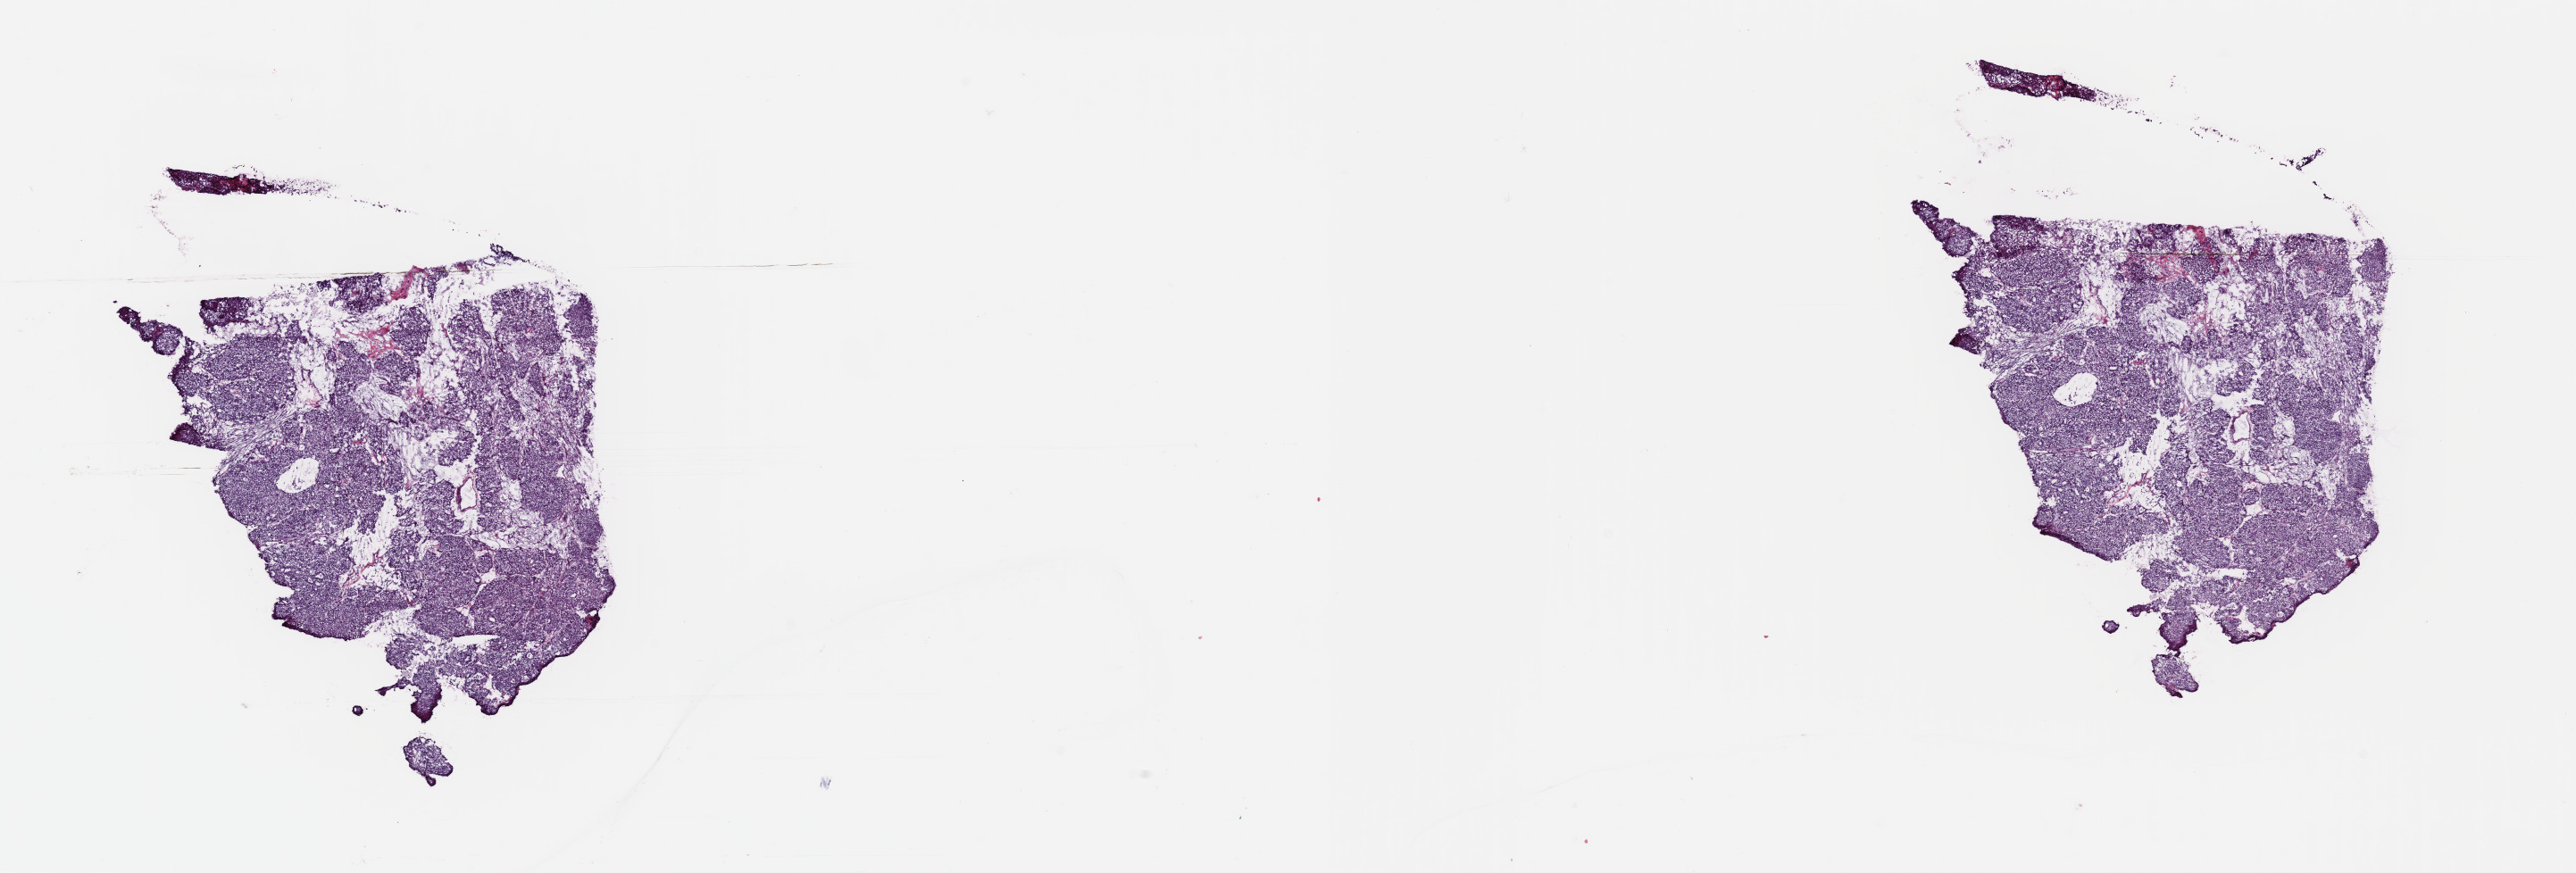
Digitized Hematoxylin and eosin (H&E) stained tissue section (whole slide) — low-resolution overview of the scanned area, about 22.8 x 7.7 mm, frozen section from the top of the tissue portion, uterus, primary tumour sample. Female, age 86 years at initial diagnosis. Histologic grade: G3 (poorly differentiated). Composition of this section per pathologist review: tumour cells 80%, tumour nuclei 80%, normal cells 0%, stromal cells 18%, necrosis 2%. Infiltration values recorded for this section: lymphocyte infiltration 0%, monocyte infiltration 0%, neutrophil infiltration 0%.
FIGO stage: IA. Diagnosis: Endometrioid adenocarcinoma, NOS.